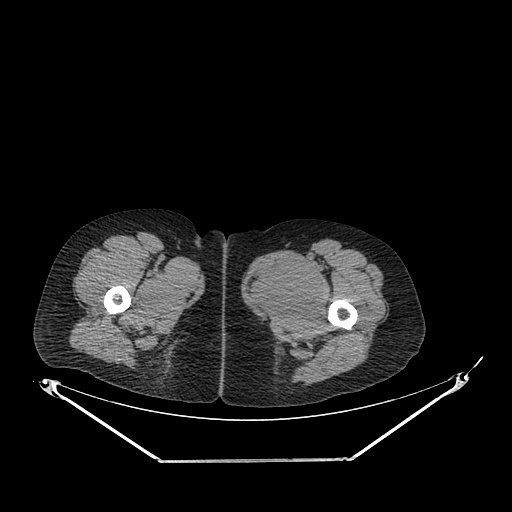
CT of an extremity soft-tissue mass (from a PET/CT study), one axial slice. Slice 251 of 267 in the series (ordered by position). Soft-tissue window (W 400 / L 40 HU). 512 × 512 image matrix, field of view 500 × 500 mm. Female patient. Case-level facts recorded for this patient, not image findings: histological type: pleiomorphic leiomyosarcoma; grade: intermediate; site of the primary tumour: left thigh.
Structures marked on this image (expert contour drawn on MRI and transferred to this co-registered scan by the dataset authors):
- gross tumour volume including surrounding oedema: box from (x=247, y=253) to (x=321, y=316) px
- gross tumour volume (mass): (x=247, y=253)–(x=321, y=316)